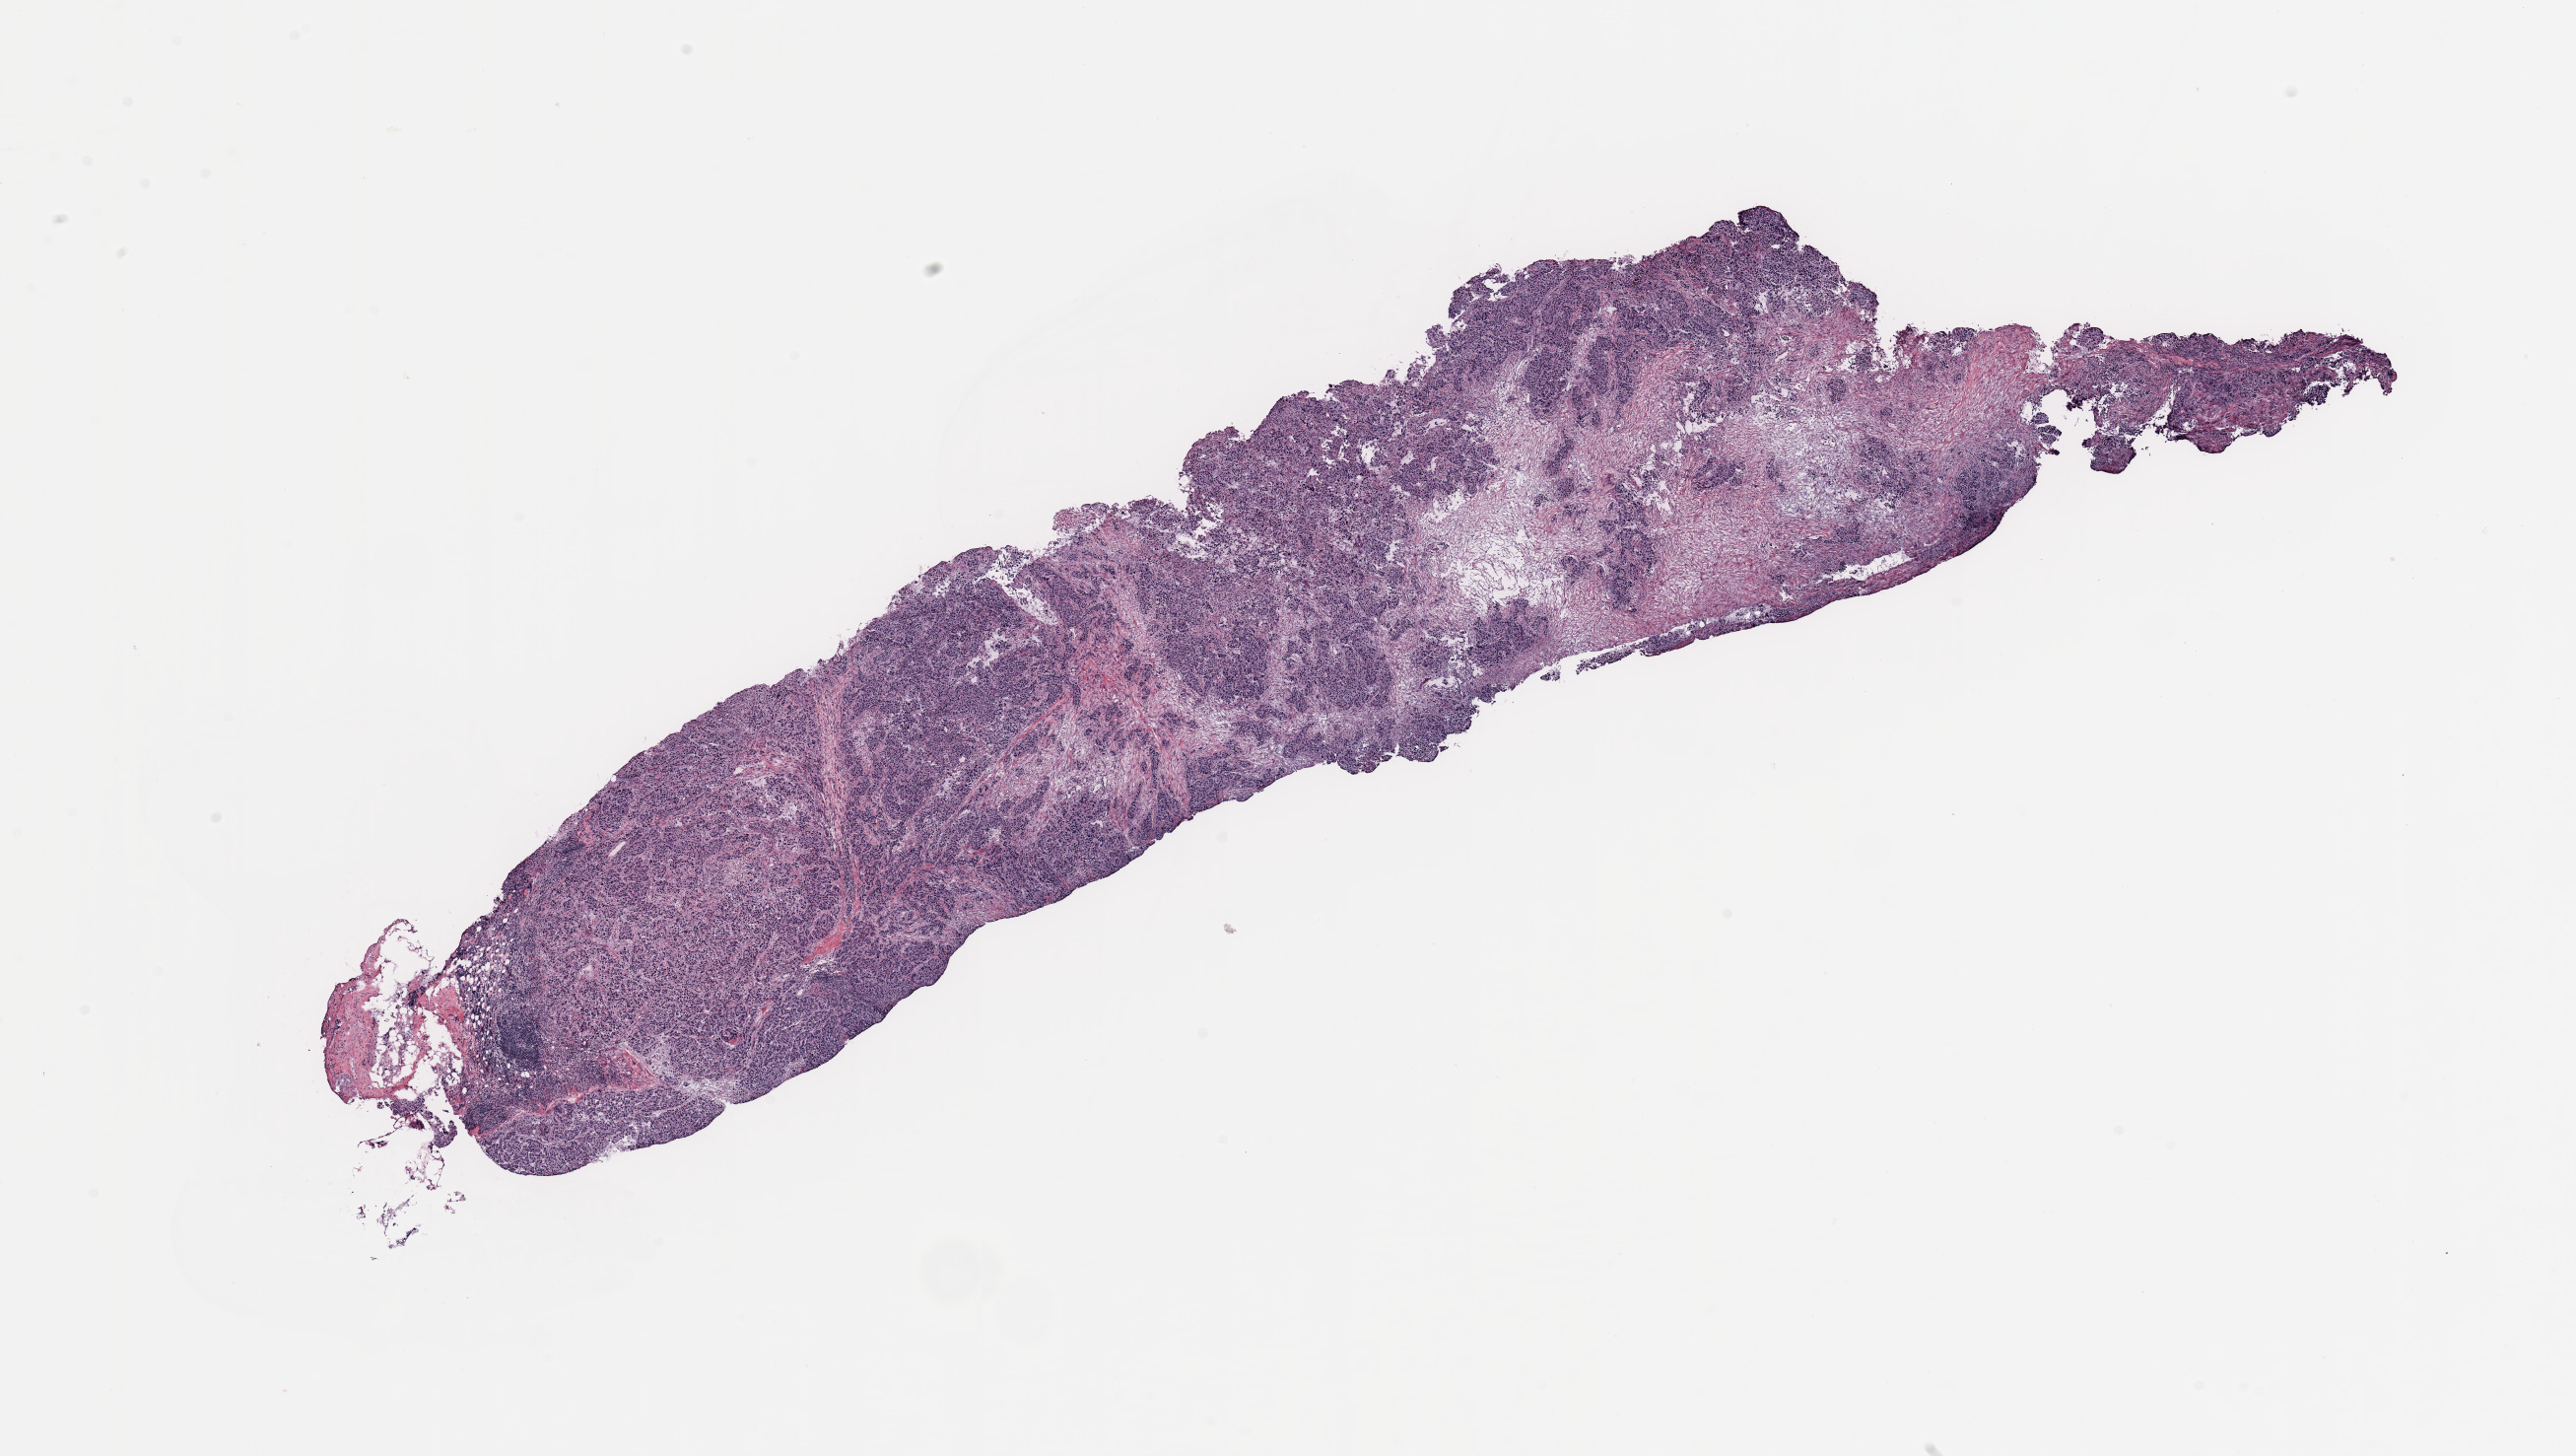
Whole-slide histology image, H&E-stained, a low-resolution overview of the entire scanned area, about 20.7 x 11.7 mm (from a 20x scan). Tumour tissue sample, breast. 80-year-old female patient.
Histologic diagnosis: Infiltrating duct carcinoma, NOS.